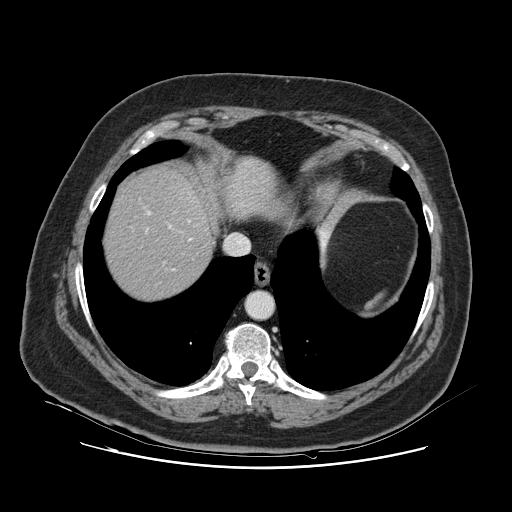
Contrast-enhanced abdominal CT, one axial slice; slice 107 of 132 in the series (ordered by position); intravenous contrast given; soft-tissue window (W 400 / L 40 HU); 512 × 512 image matrix, field of view 391 × 391 mm. Female patient, age 73 years. Case-level facts recorded for this patient, not image findings: diagnosis: colorectal cancer liver metastases, imaged before liver resection; multiple liver metastases: no; largest metastasis: 7 cm; disease in both lobes: no.
Annotated regions visible in this slice (expert manual segmentation):
- hepatic veins: bounding box [x1, y1, x2, y2] px = [146, 211, 191, 271]
- liver: [105, 171, 212, 299]
- planned liver remnant (the part of the liver to remain after resection): [106, 171, 211, 300]
- portal vein (with intrahepatic branches): [168, 225, 171, 228]